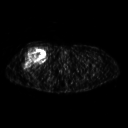
FDG PET of an extremity soft-tissue mass (from a PET/CT study), one axial slice; position 268 of 311 along the scan axis; 3.27 mm slice thickness; 128 × 128 image matrix. Patient: female, 57 years. Case-level facts recorded for this patient, not image findings: histological type: pleiomorphic undifferentiated sarcoma; grade: high; site of the primary tumour: right quadricep.
Annotated regions visible in this slice (expert contour drawn on MRI and transferred to this co-registered scan by the dataset authors):
- tumour plus oedema (research contour): bounding box (x1, y1, x2, y2) in pixels: (23, 47, 46, 69)
- tumour (research contour): (23, 47, 46, 69)